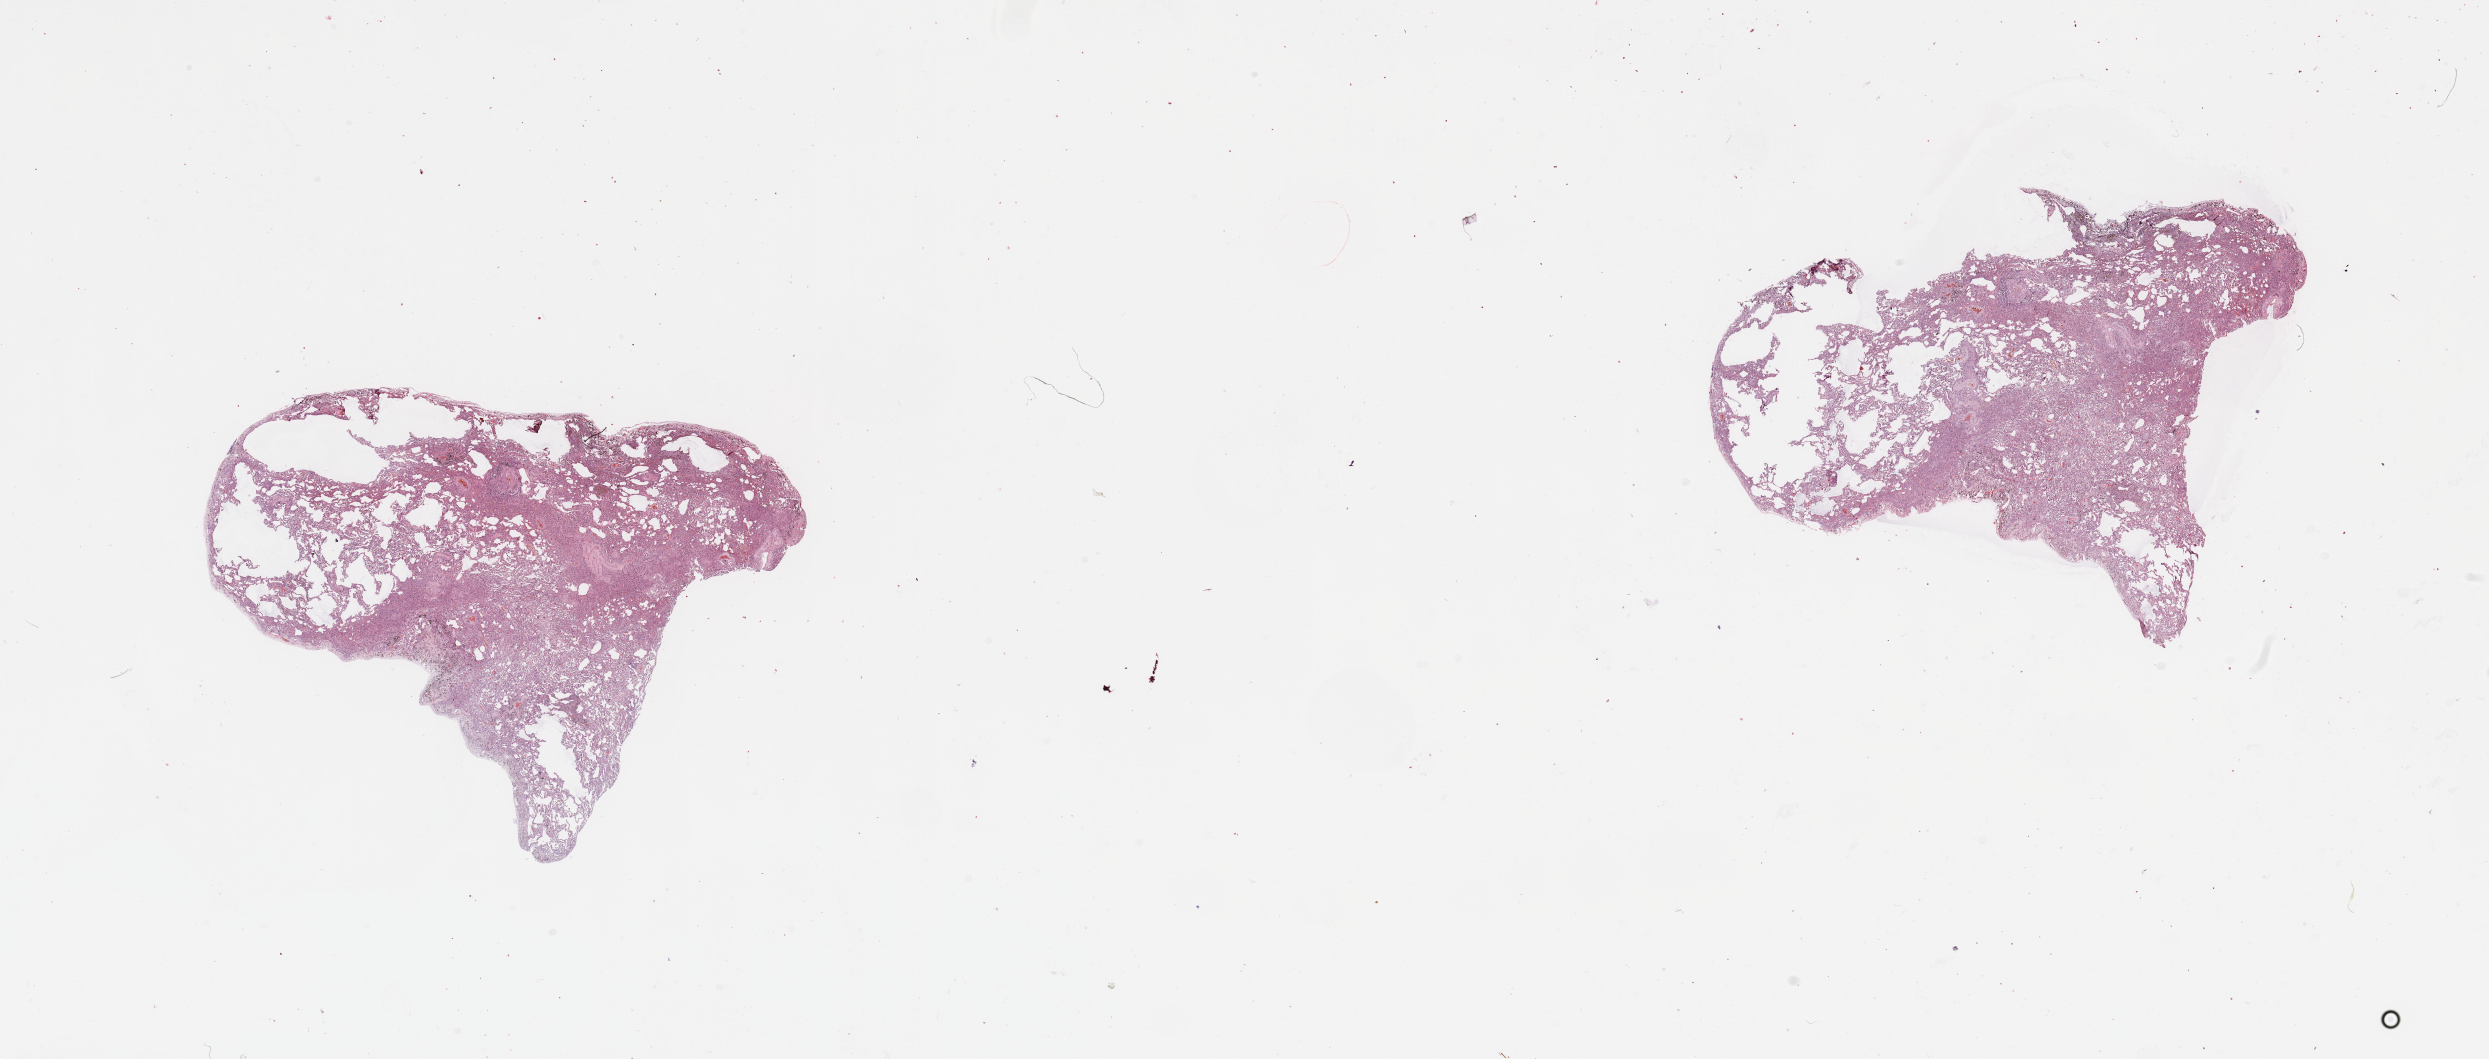
Digitized H&E tissue section (whole slide), shown as a low-resolution overview of the whole scanned area (about 39.4 x 16.8 mm, from a 20x scan). Normal (non-tumour) tissue sample, lung. Patient: male, age 65 years.
* this section: normal (non-tumour) tissue from the same patient
* patient diagnosis: Squamous cell carcinoma, NOS